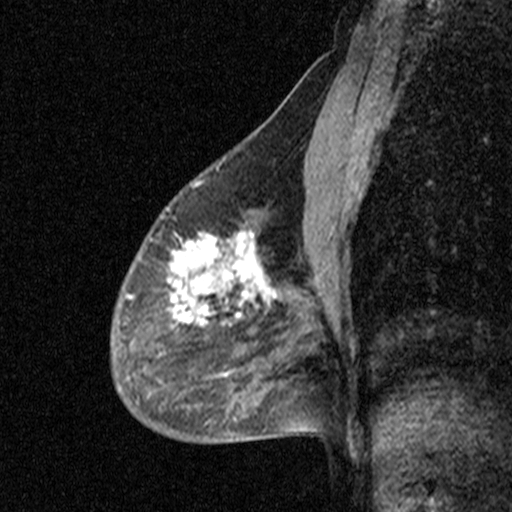
Breast MRI (dynamic contrast-enhanced), one sagittal slice; position 27 of 44 along the scan axis; dynamic contrast-enhanced study with each time point stored as its own series, time point 2 of 3 at this slice position (early post-contrast, ordered by acquisition time); 1.5 T; TE 4.5 ms, TR 11 ms; 512 × 512 image matrix, field of view 200 × 200 mm. Female patient, age 53 years. Case-level facts recorded for this patient, not image findings: setting: breast cancer imaged before/during neoadjuvant chemotherapy; receptor status: HR-positive, HER2-negative.
Outlined on this slice (semi-automatically segmented with operator editing):
- analysis volume of interest (the breast-tissue region the enhancement analysis was run in; not a lesion): bounding box <88,176,313,423> (left, top, right, bottom; pixels)
- tumour enhancement mask (voxels above the 90 % enhancement threshold inside the analysis volume of interest): <171,231,277,325>